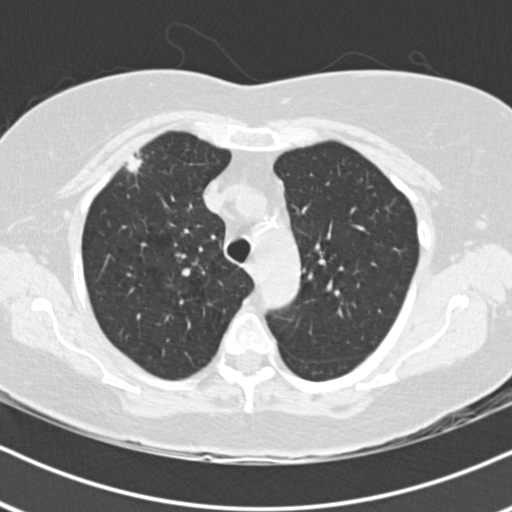
Chest CT (low-dose screening protocol), one axial image; first (baseline) screen; lung window (W 1500 / L -600 HU); standard (soft-tissue) reconstruction kernel (B30f); slice 42 of 178 in the series; 512 × 512 image matrix, field of view 320 × 320 mm. Female, age 74 years at enrolment. Former smoker at enrolment.
• Expert reader's lesion annotation, box from (x=105, y=139) to (x=160, y=193) px.
• The exam's reader record, not a measurement of the box and not confirmed to be the same lesion: non-calcified nodule or mass ≥4 mm, right upper lobe, 16 × 10 mm, poorly defined margins, soft tissue attenuation.
• Participant outcome: lung cancer diagnosed 33 days after this screen — adenocarcinoma, NOS, right upper lobe, poorly differentiated (G3), stage IIIA (AJCC 6th edition), 24 mm at pathology.